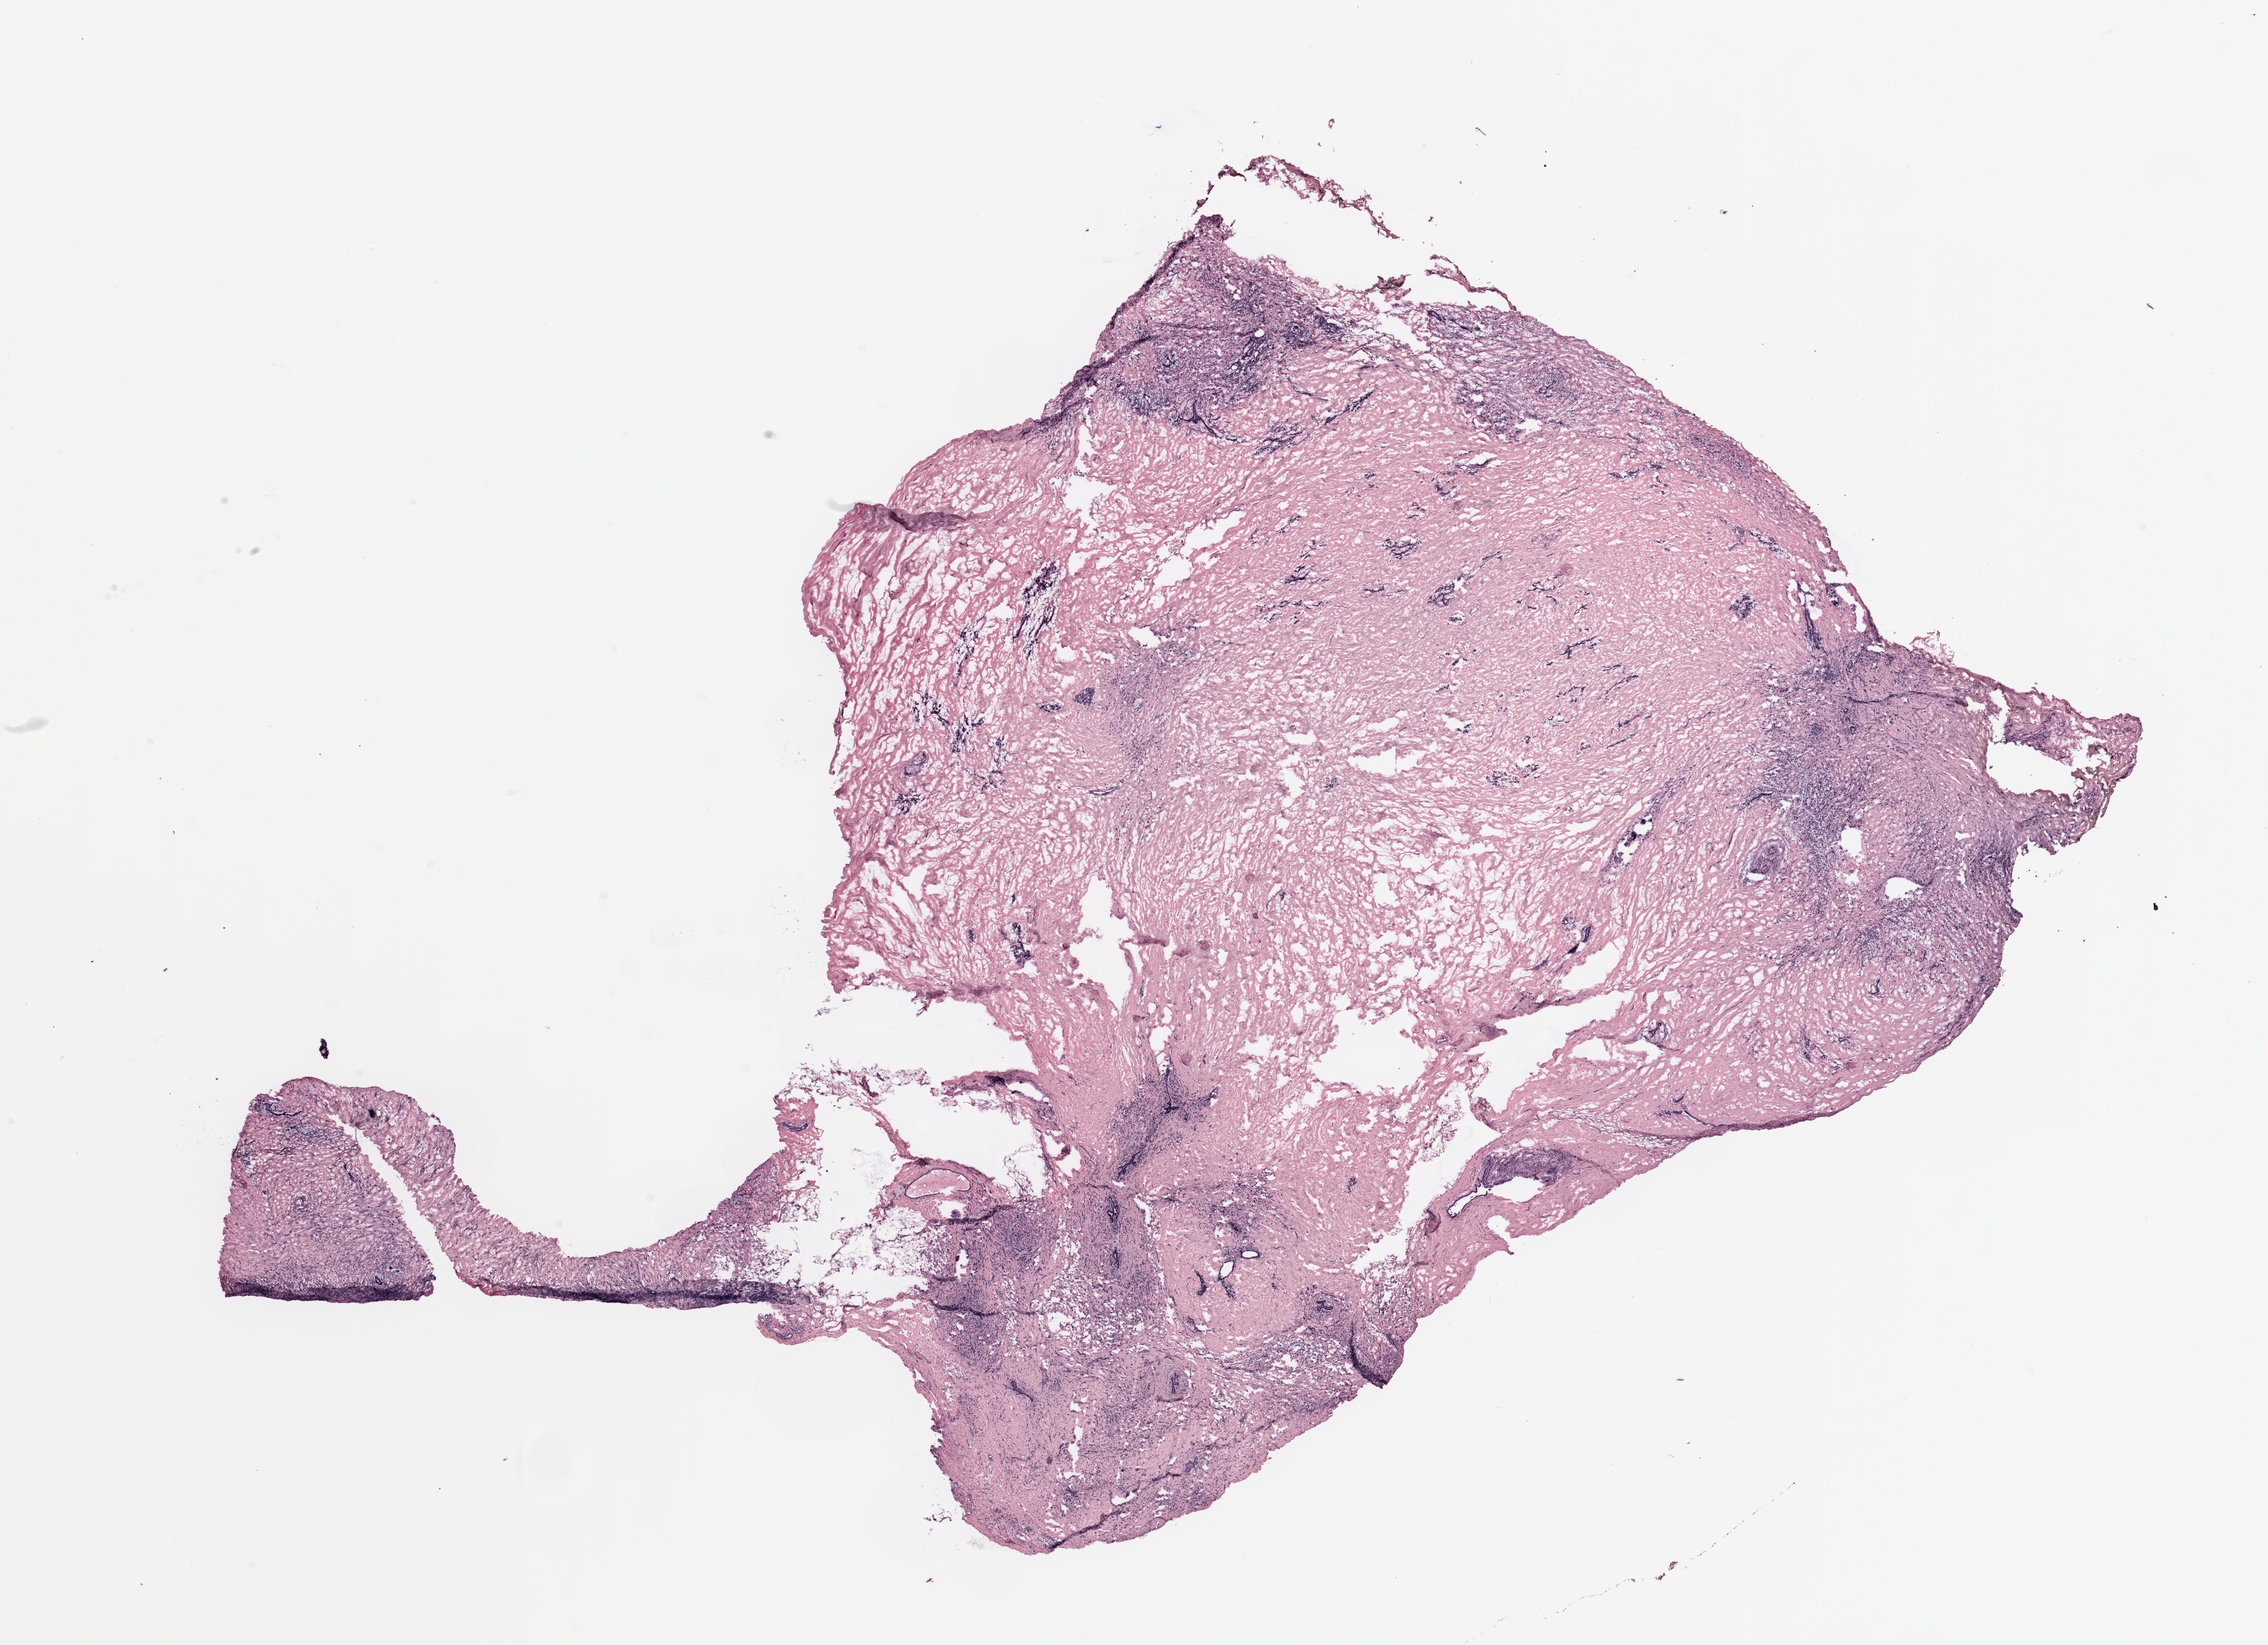
Digitized H&E tissue section (whole slide), low-resolution overview of the scanned area, about 25.6 x 18.6 mm; breast, tissue type not recorded.
Patient diagnosis (cohort enrolment): breast cancer (breast).